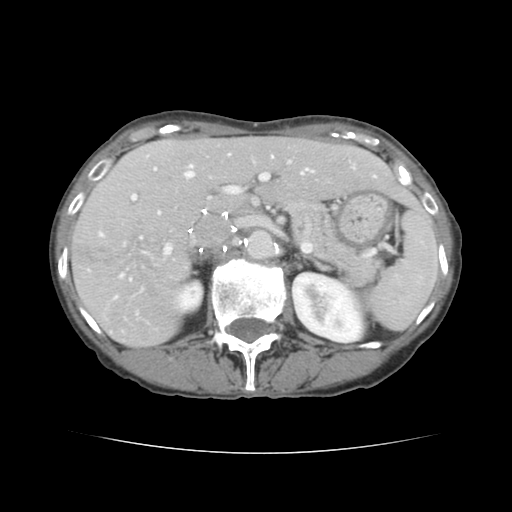
Contrast-enhanced abdominal CT, one axial slice; slice 84 of 136 in the series (ordered by position); 120 kVp; soft-tissue window (W 400 / L 40 HU); 512 × 512 image matrix. Female patient, age 77 years. From the clinical record (not read from this slice): diagnosis: colorectal cancer liver metastases, imaged before liver resection; multiple liver metastases: yes; largest metastasis: 3 cm; disease in both lobes: no.
Annotated regions visible in this slice (manually delineated by an expert):
- hepatic veins: box from (x=140, y=154) to (x=308, y=238) px
- liver: (x=73, y=137)–(x=416, y=346)
- planned liver remnant (the part of the liver to remain after resection): (x=154, y=137)–(x=416, y=211)
- portal vein (with intrahepatic branches): (x=99, y=161)–(x=354, y=280)
- liver metastasis: (x=74, y=246)–(x=98, y=264)